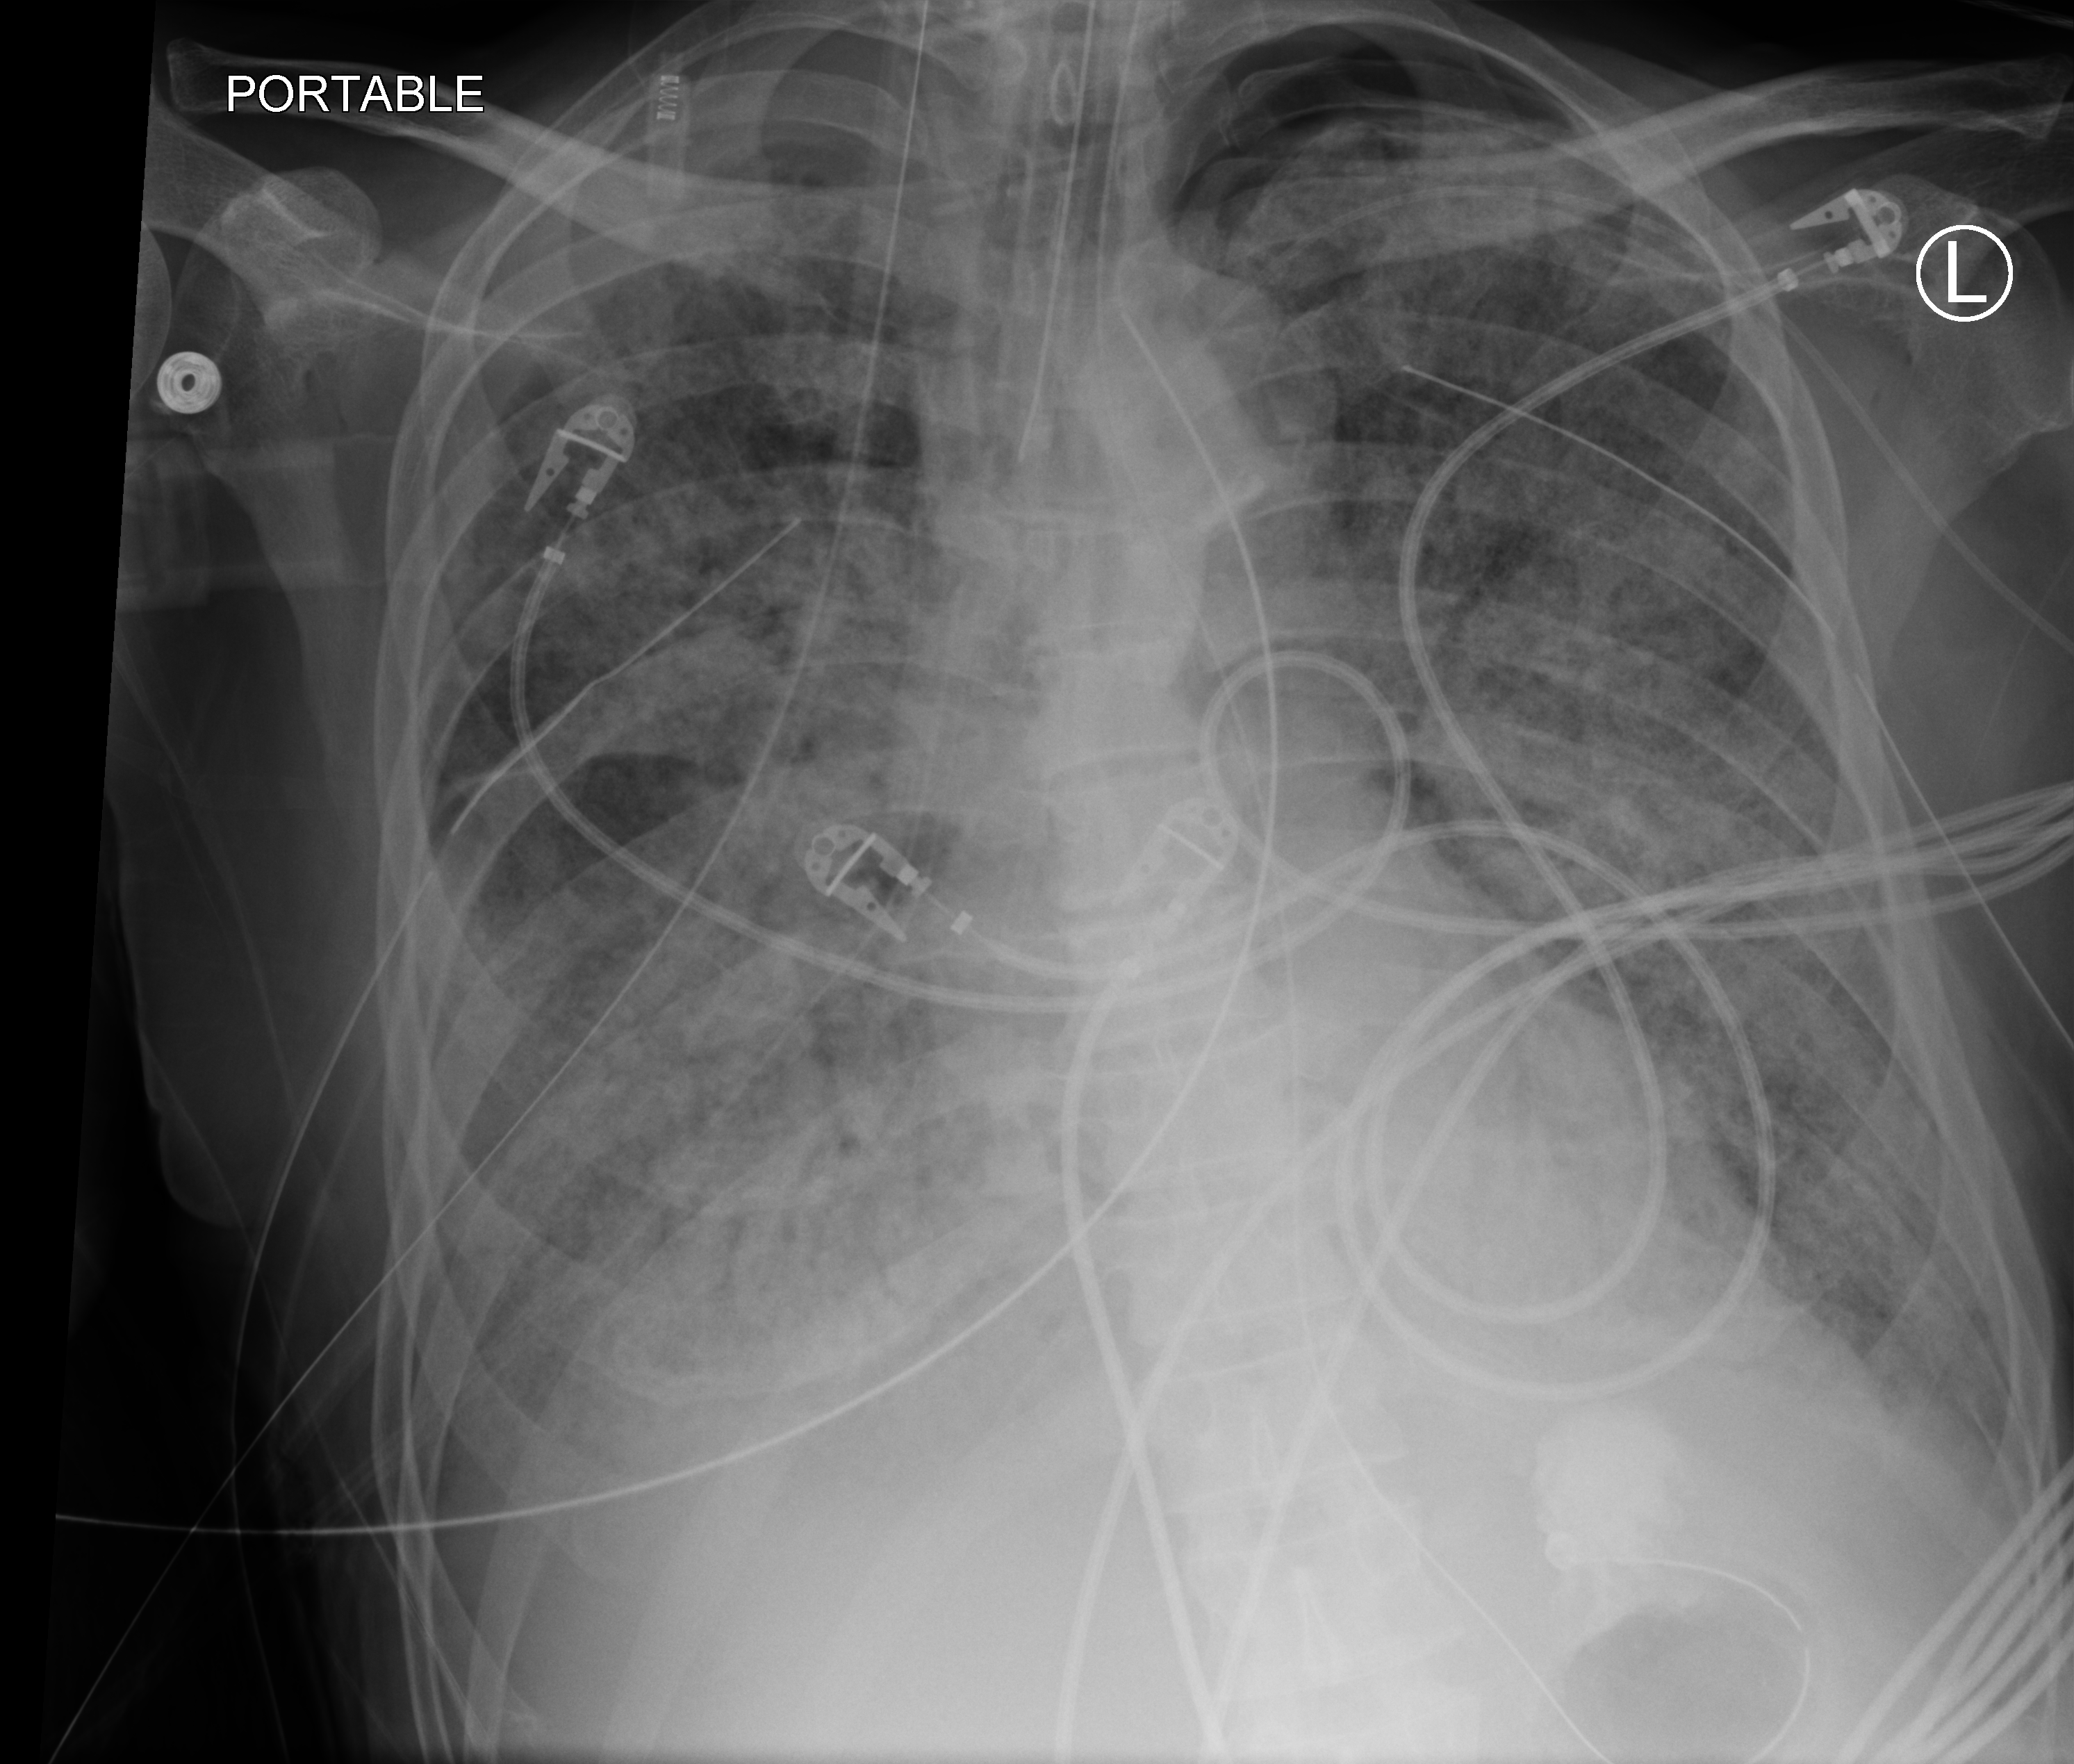
Chest X-ray (portable); anteroposterior (AP) projection. Male patient hospitalised with COVID-19, age 60–74 years.
Admission-level facts for this patient (not findings on this image; timing relative to this image not recorded): COPD (admission record): no.